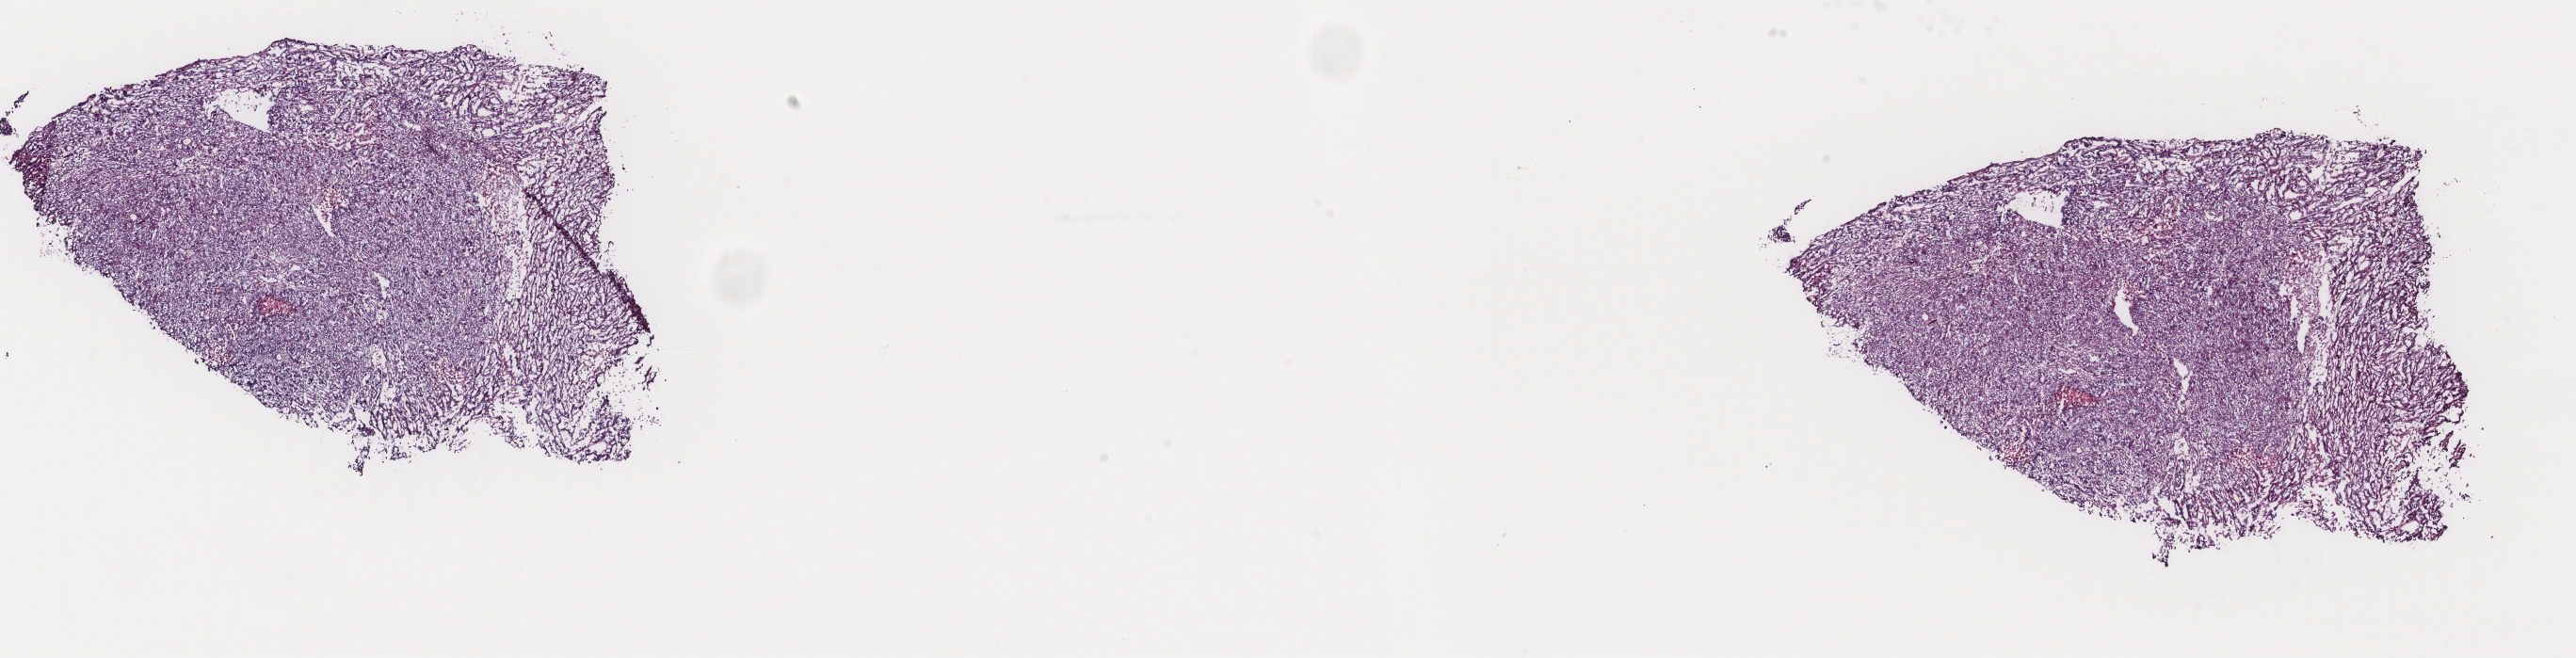
Digitized Hematoxylin and eosin (H&E) stained tissue section (whole slide) — a low-resolution overview of the entire scanned area, about 21.7 x 5.5 mm; frozen section from the top of the tissue portion; sample: primary tumour, uterus. Patient: female, age at initial diagnosis 60 years. Histologic grade: G3 (poorly differentiated). Pathologist review of this section (percent, as recorded): tumour cells 95%, tumour nuclei 95%, normal cells 0%, stromal cells 3%, necrosis 2%. Inflammatory infiltration, as recorded: lymphocyte infiltration 50%, monocyte infiltration 10%, neutrophil infiltration 20%.
Pathologic diagnosis: Serous cystadenocarcinoma, NOS (endometrium). FIGO stage: IVB.